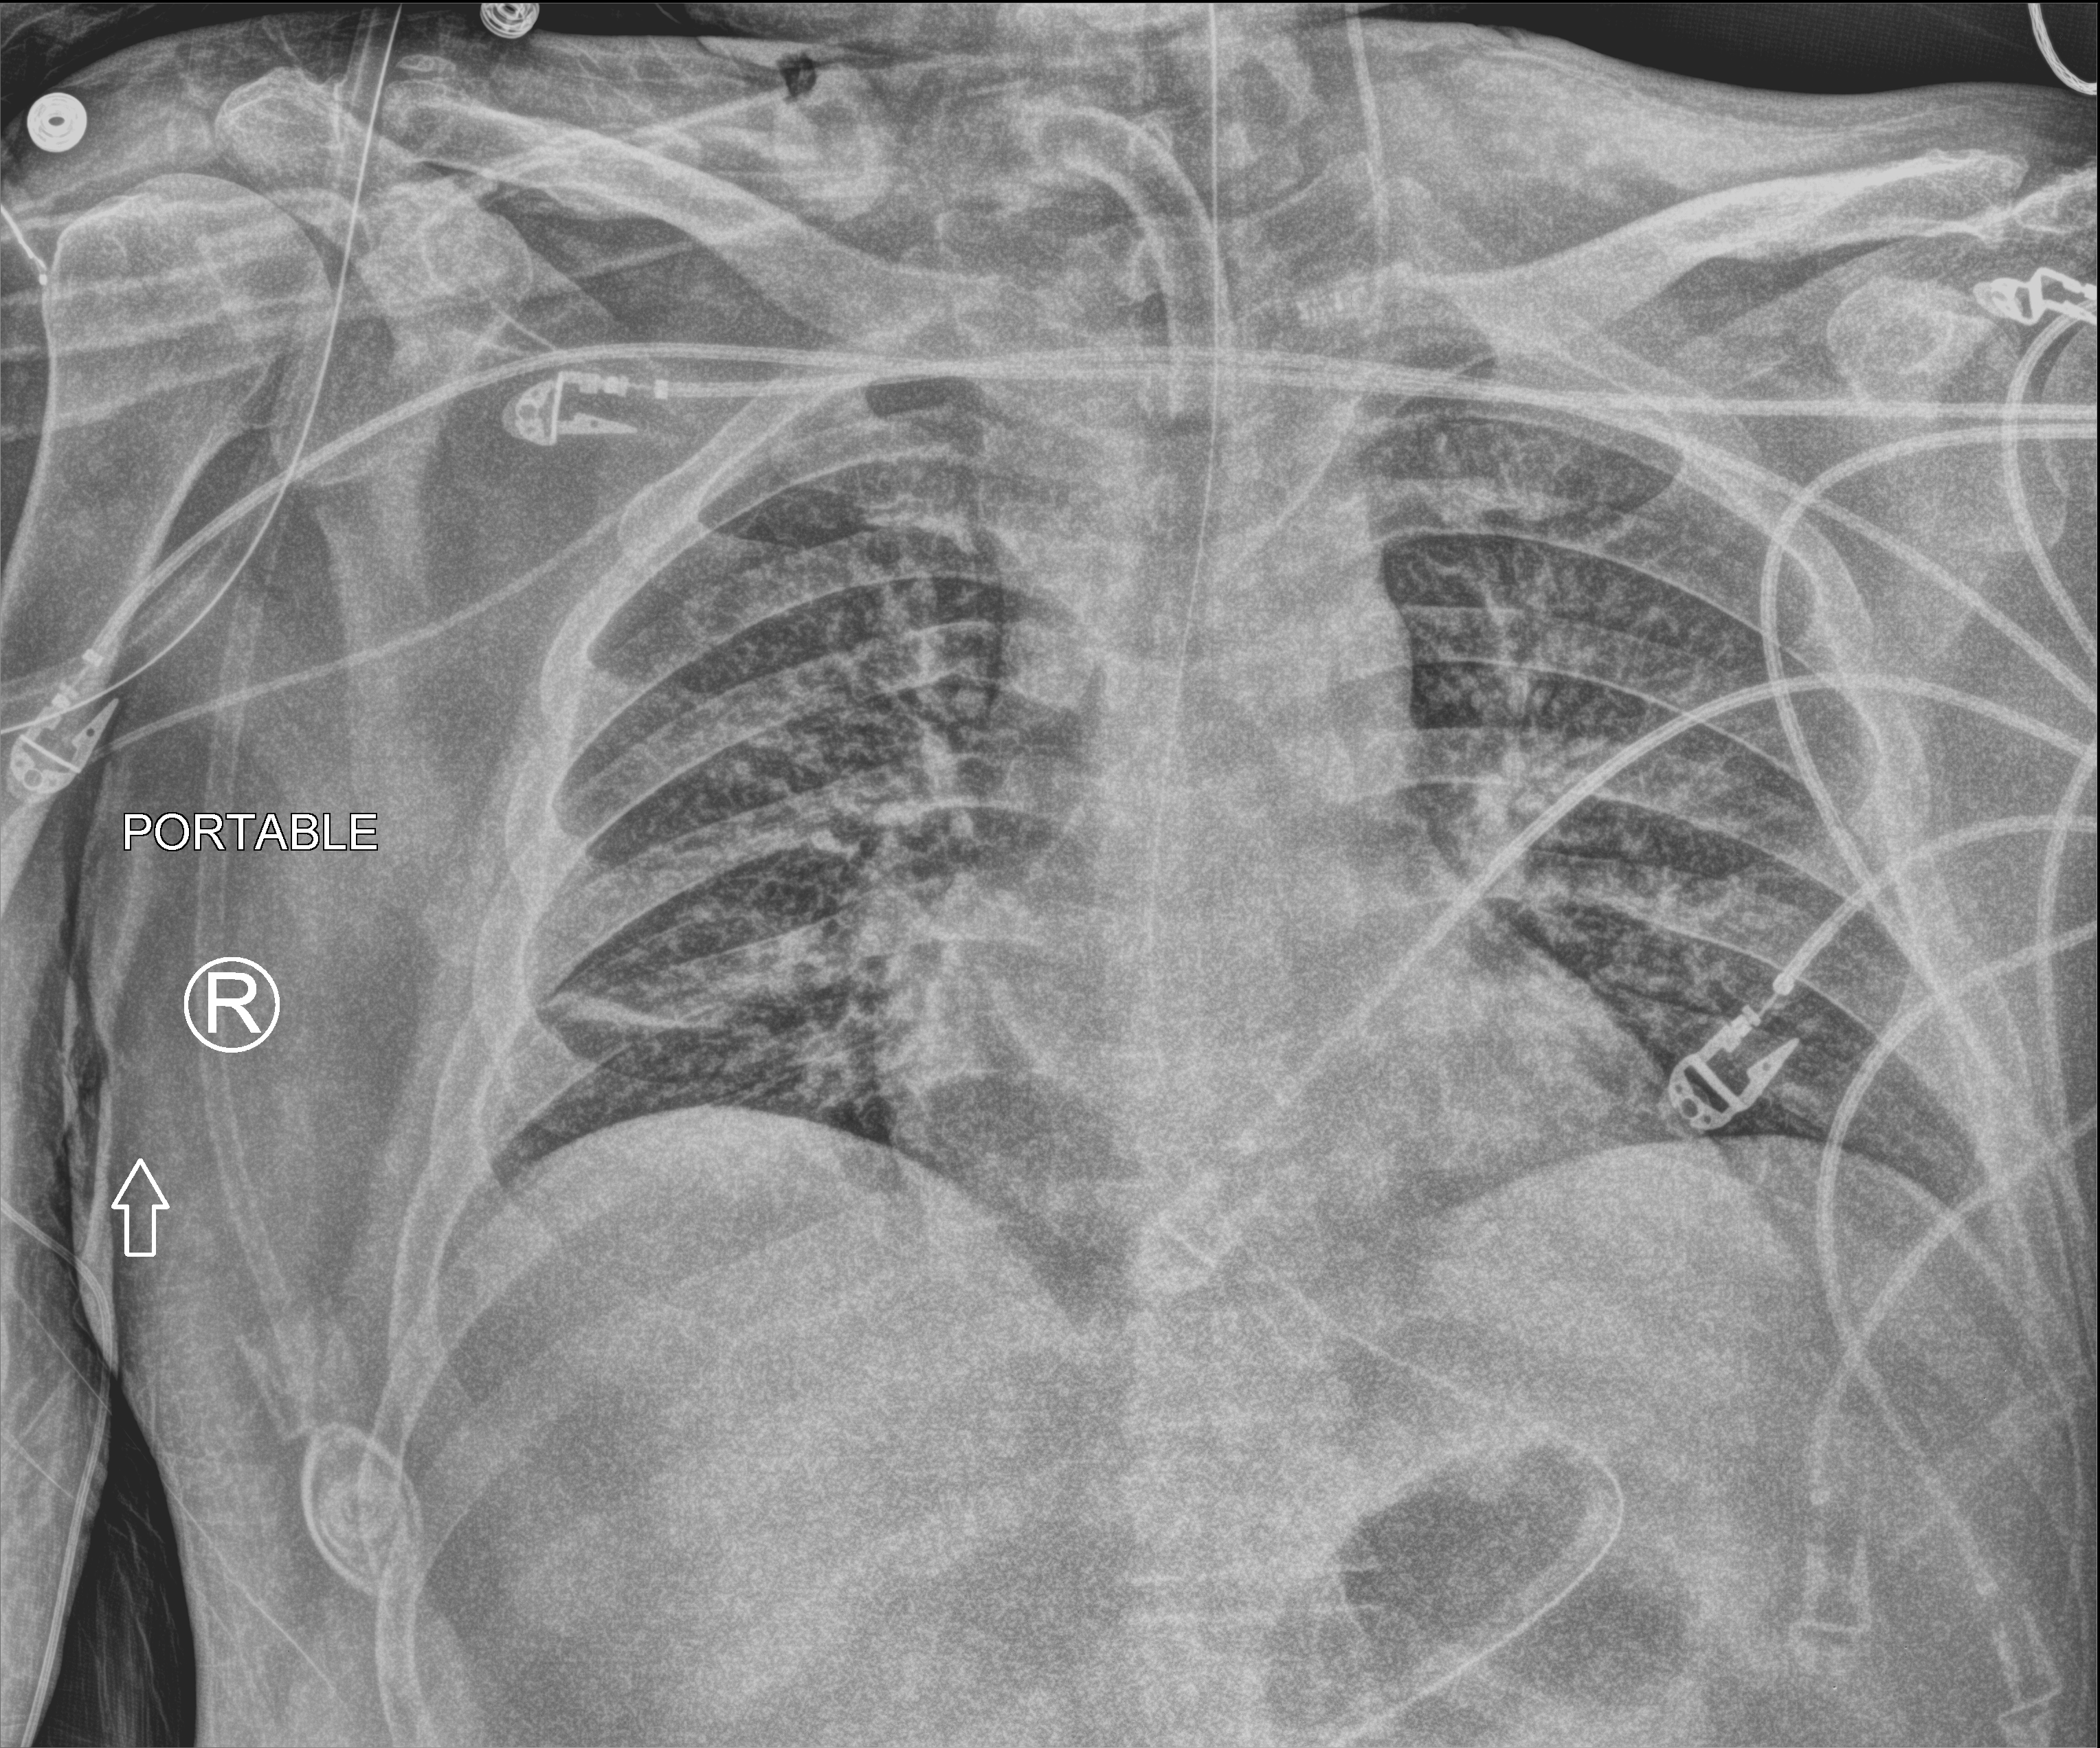
Portable chest radiograph; anteroposterior (AP) projection. Male patient hospitalised with COVID-19, age 18–59 years.
From the hospital-stay record, not from the radiograph (when in the stay this image was taken is not recorded): admitted to intensive care during this hospital stay: yes.